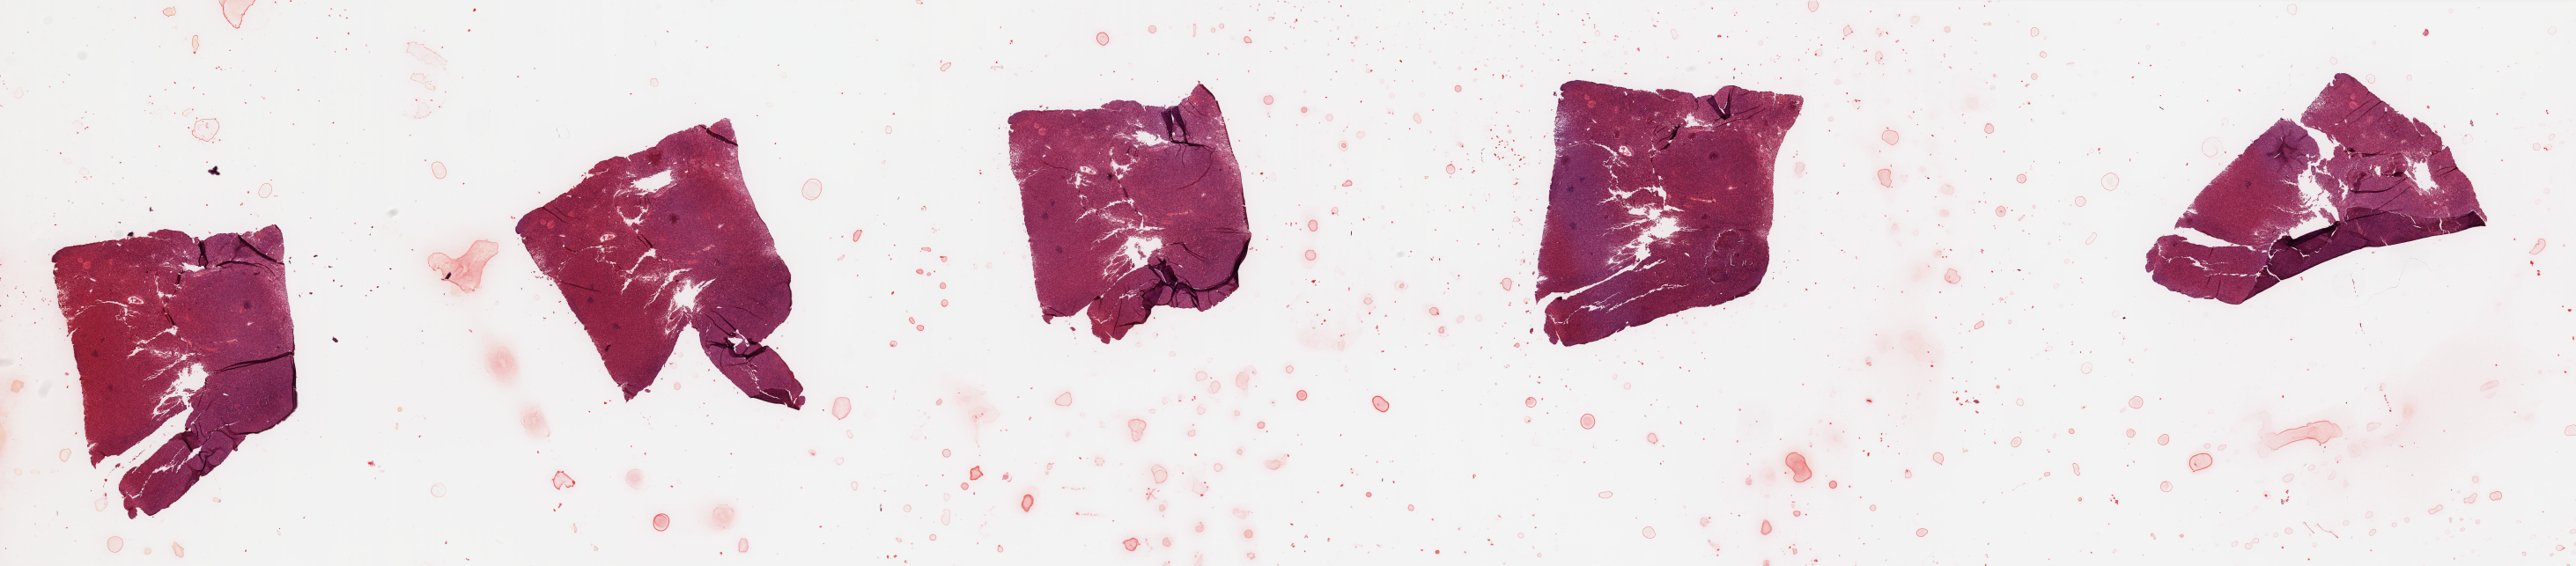
Hematoxylin and eosin (H&E) stained whole-slide image, whole scanned area (about 46.3 x 10.2 mm, slide scanned at 20x) shown as a low-resolution overview. Tumour tissue sample. 75-year-old female patient.
• patient diagnosis (cohort enrolment): sarcoma (site not recorded at cohort level)
• primary tumour site (as recorded): lower extremity